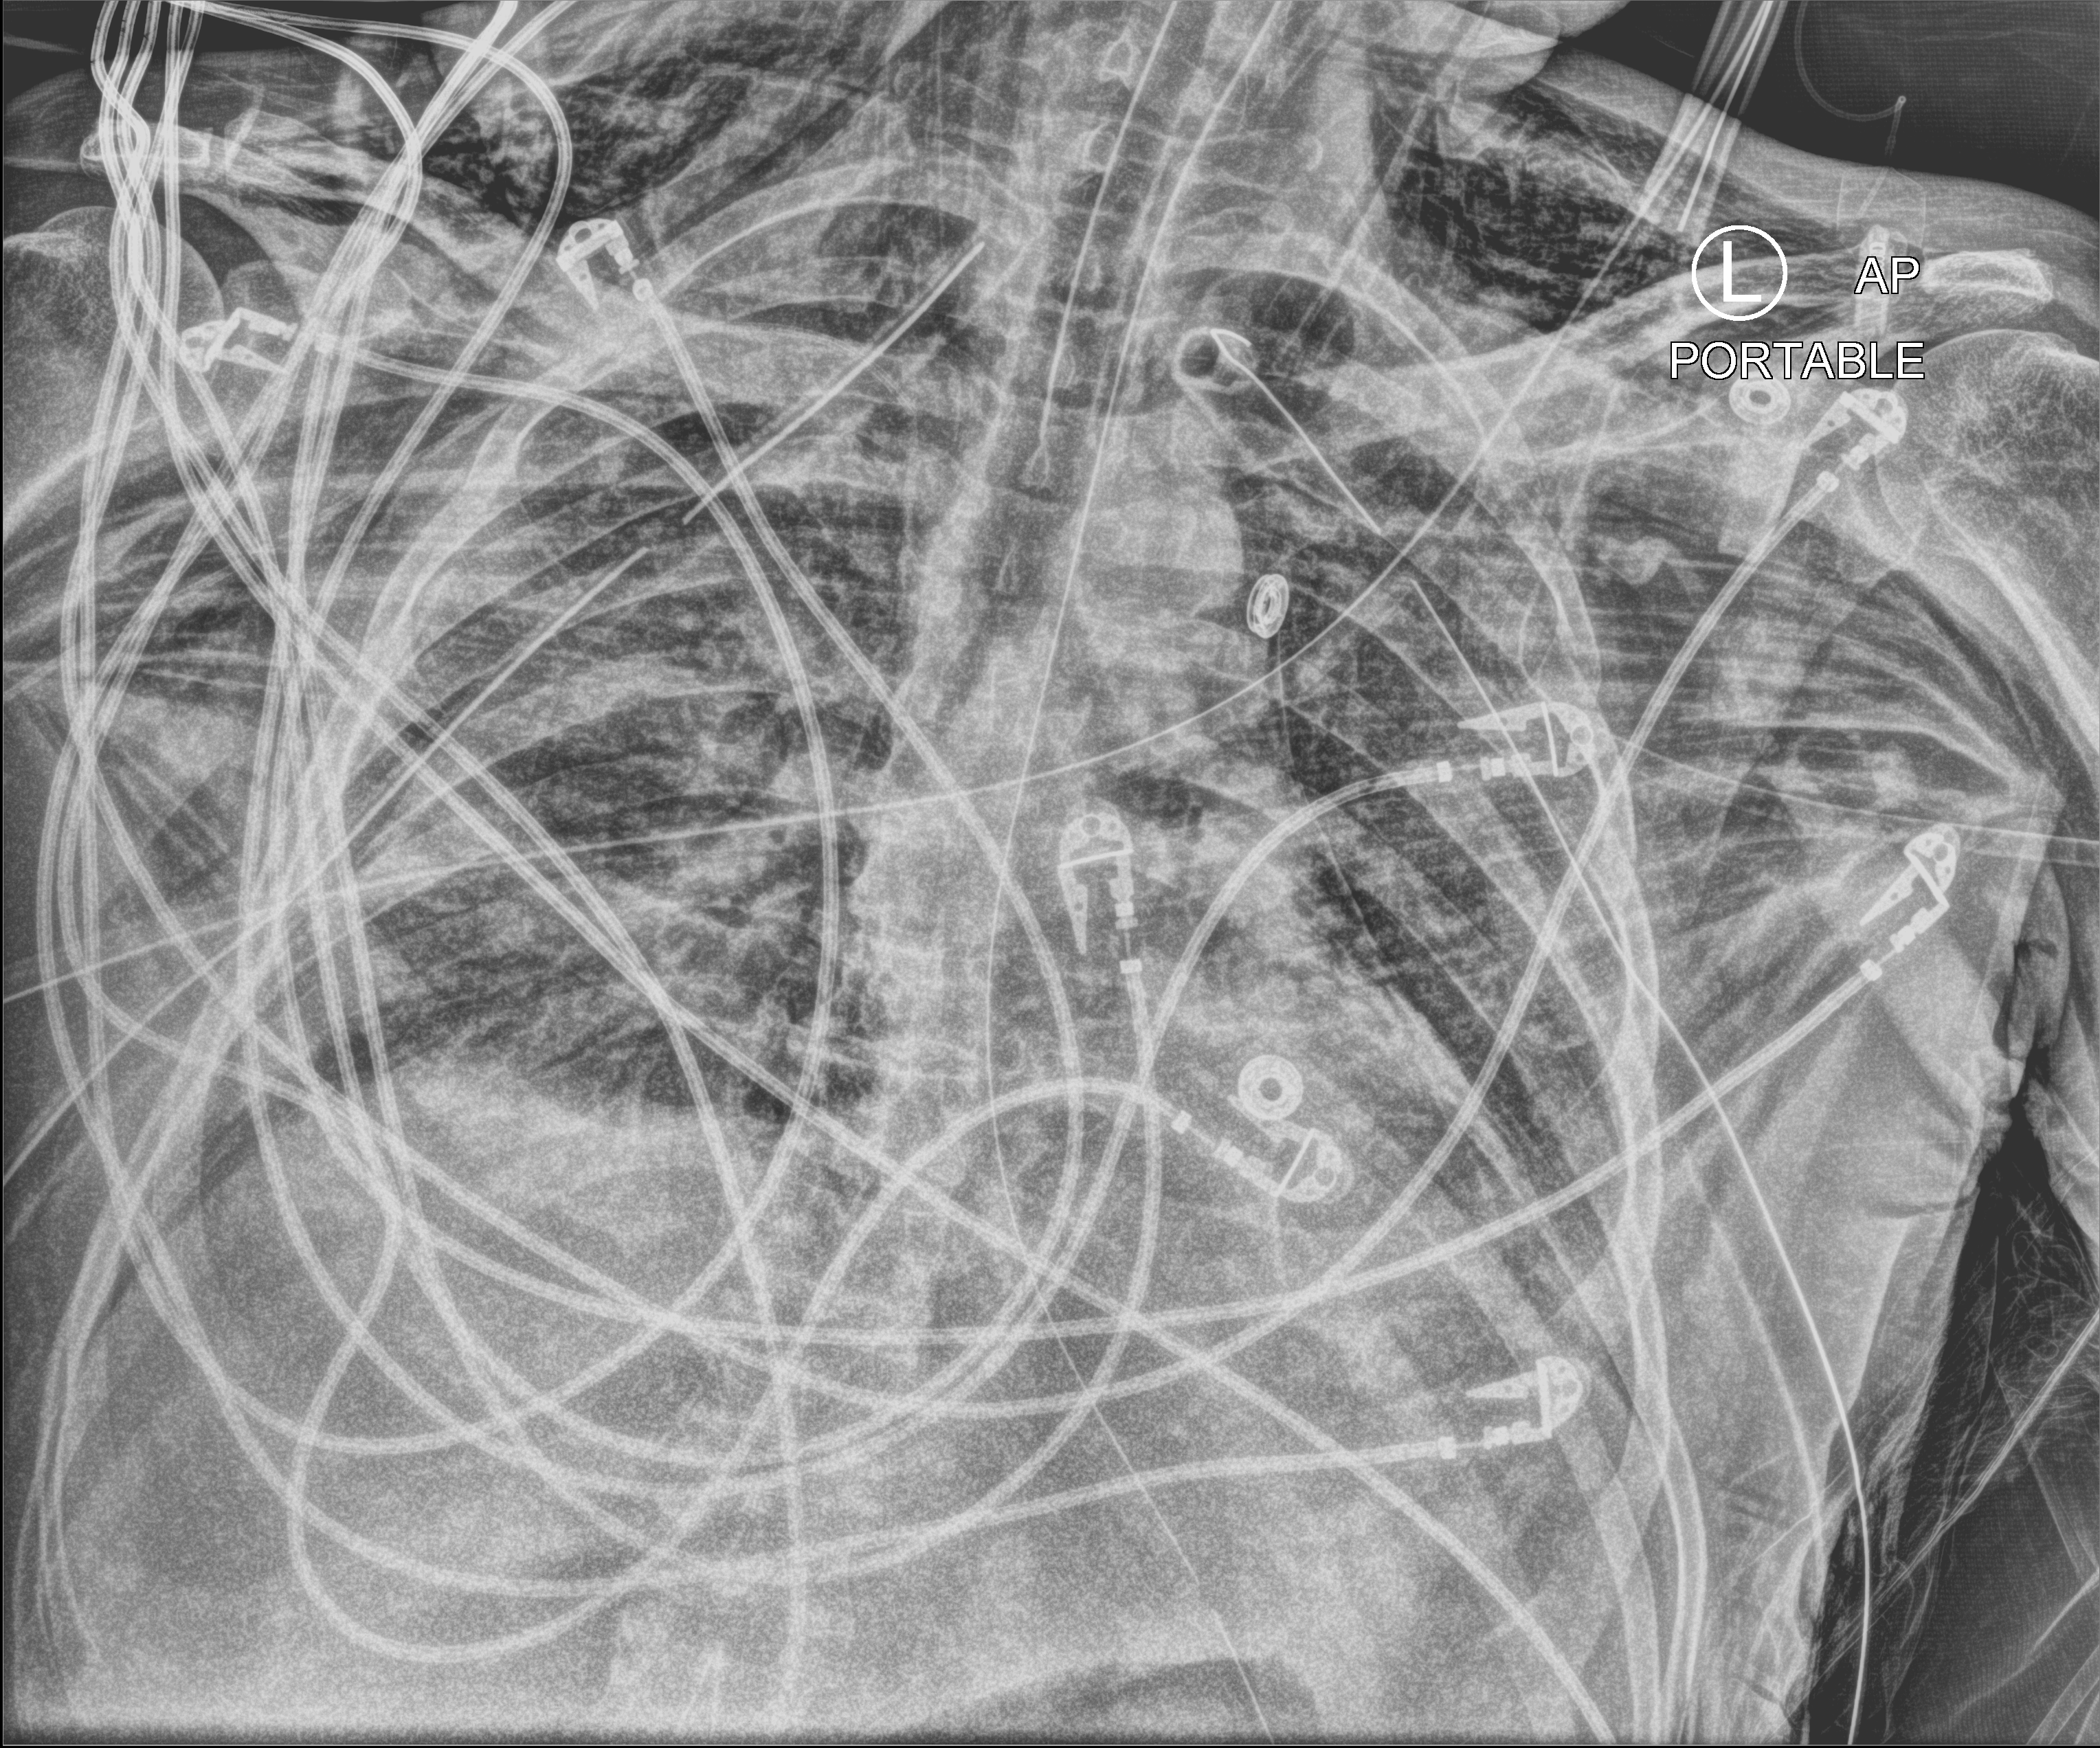
Portable chest radiograph. Patient hospitalised with COVID-19; male, aged 18–59 years.
Admission-level facts for this patient (not findings on this image; timing relative to this image not recorded):
- admitted to intensive care during this hospital stay: yes
- mechanically ventilated during this hospital stay: yes
- length of hospital stay: 83 days